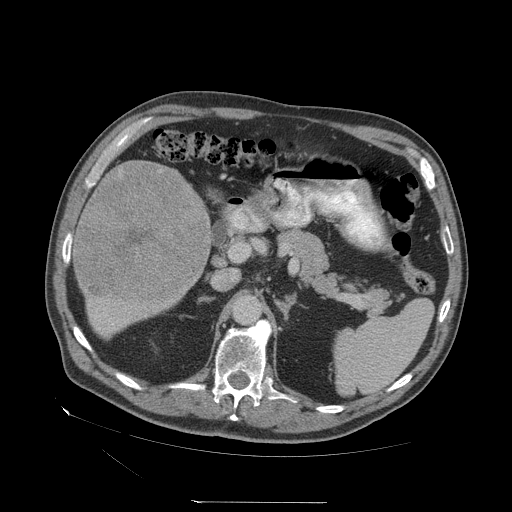
Contrast-enhanced abdominal CT (liver protocol), one axial slice; reconstruction kernel STANDARD; 140 kVp; soft-tissue window (W 400 / L 40 HU); 2.5 mm slice thickness; 512 × 512 image matrix. Case-level facts recorded for this patient, not image findings: diagnosis: hepatocellular carcinoma (patient treated with transarterial chemoembolisation; whether this scan precedes or follows treatment is not stated here); TNM stage (as recorded): Stage-I; Child-Pugh class: A.
Outlined on this slice (semi-automatic segmentation, software-assisted and operator-edited):
- liver parenchyma outside the tumour (the mass and vessels are separate outlines, so this box may not span the whole liver): bounding box <72,160,210,334> (left, top, right, bottom; pixels)
- mass: <74,160,209,302>